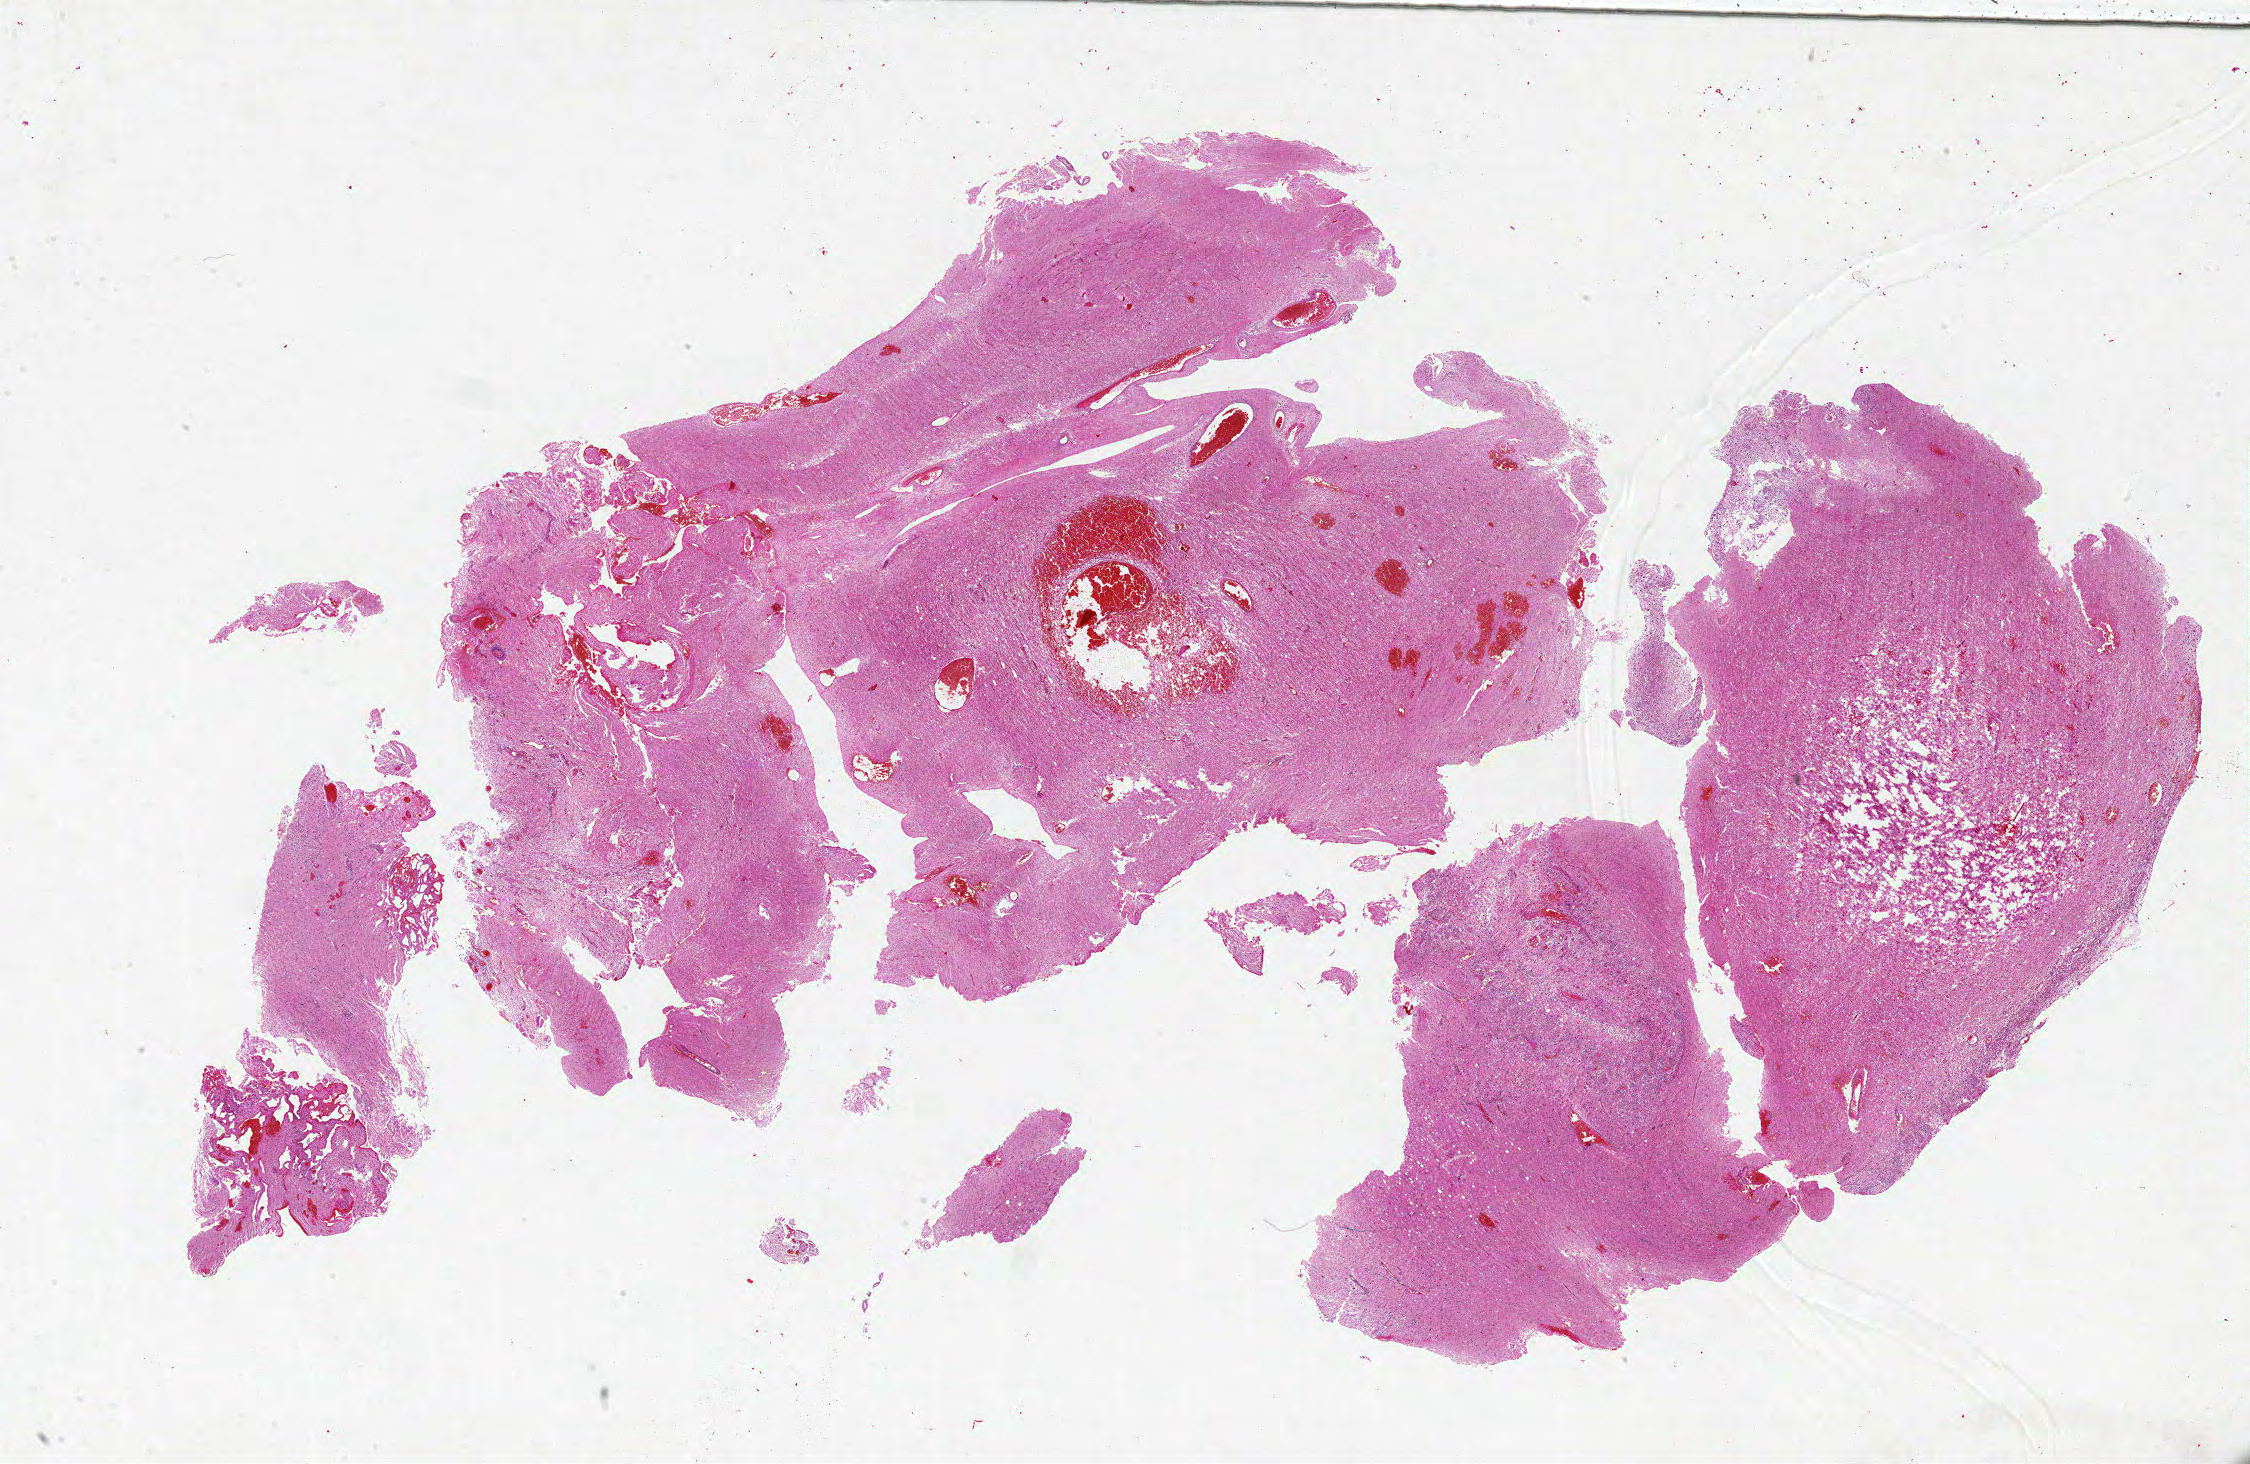
H&E-stained whole-slide image — shown as a low-resolution overview of the whole scanned area (about 36.0 x 23.4 mm, acquisition: 20x scan), formalin-fixed paraffin-embedded (FFPE) diagnostic section, primary tumour sample from the brain. Female, age 59 years at initial diagnosis.
Pathologic diagnosis: Glioblastoma.